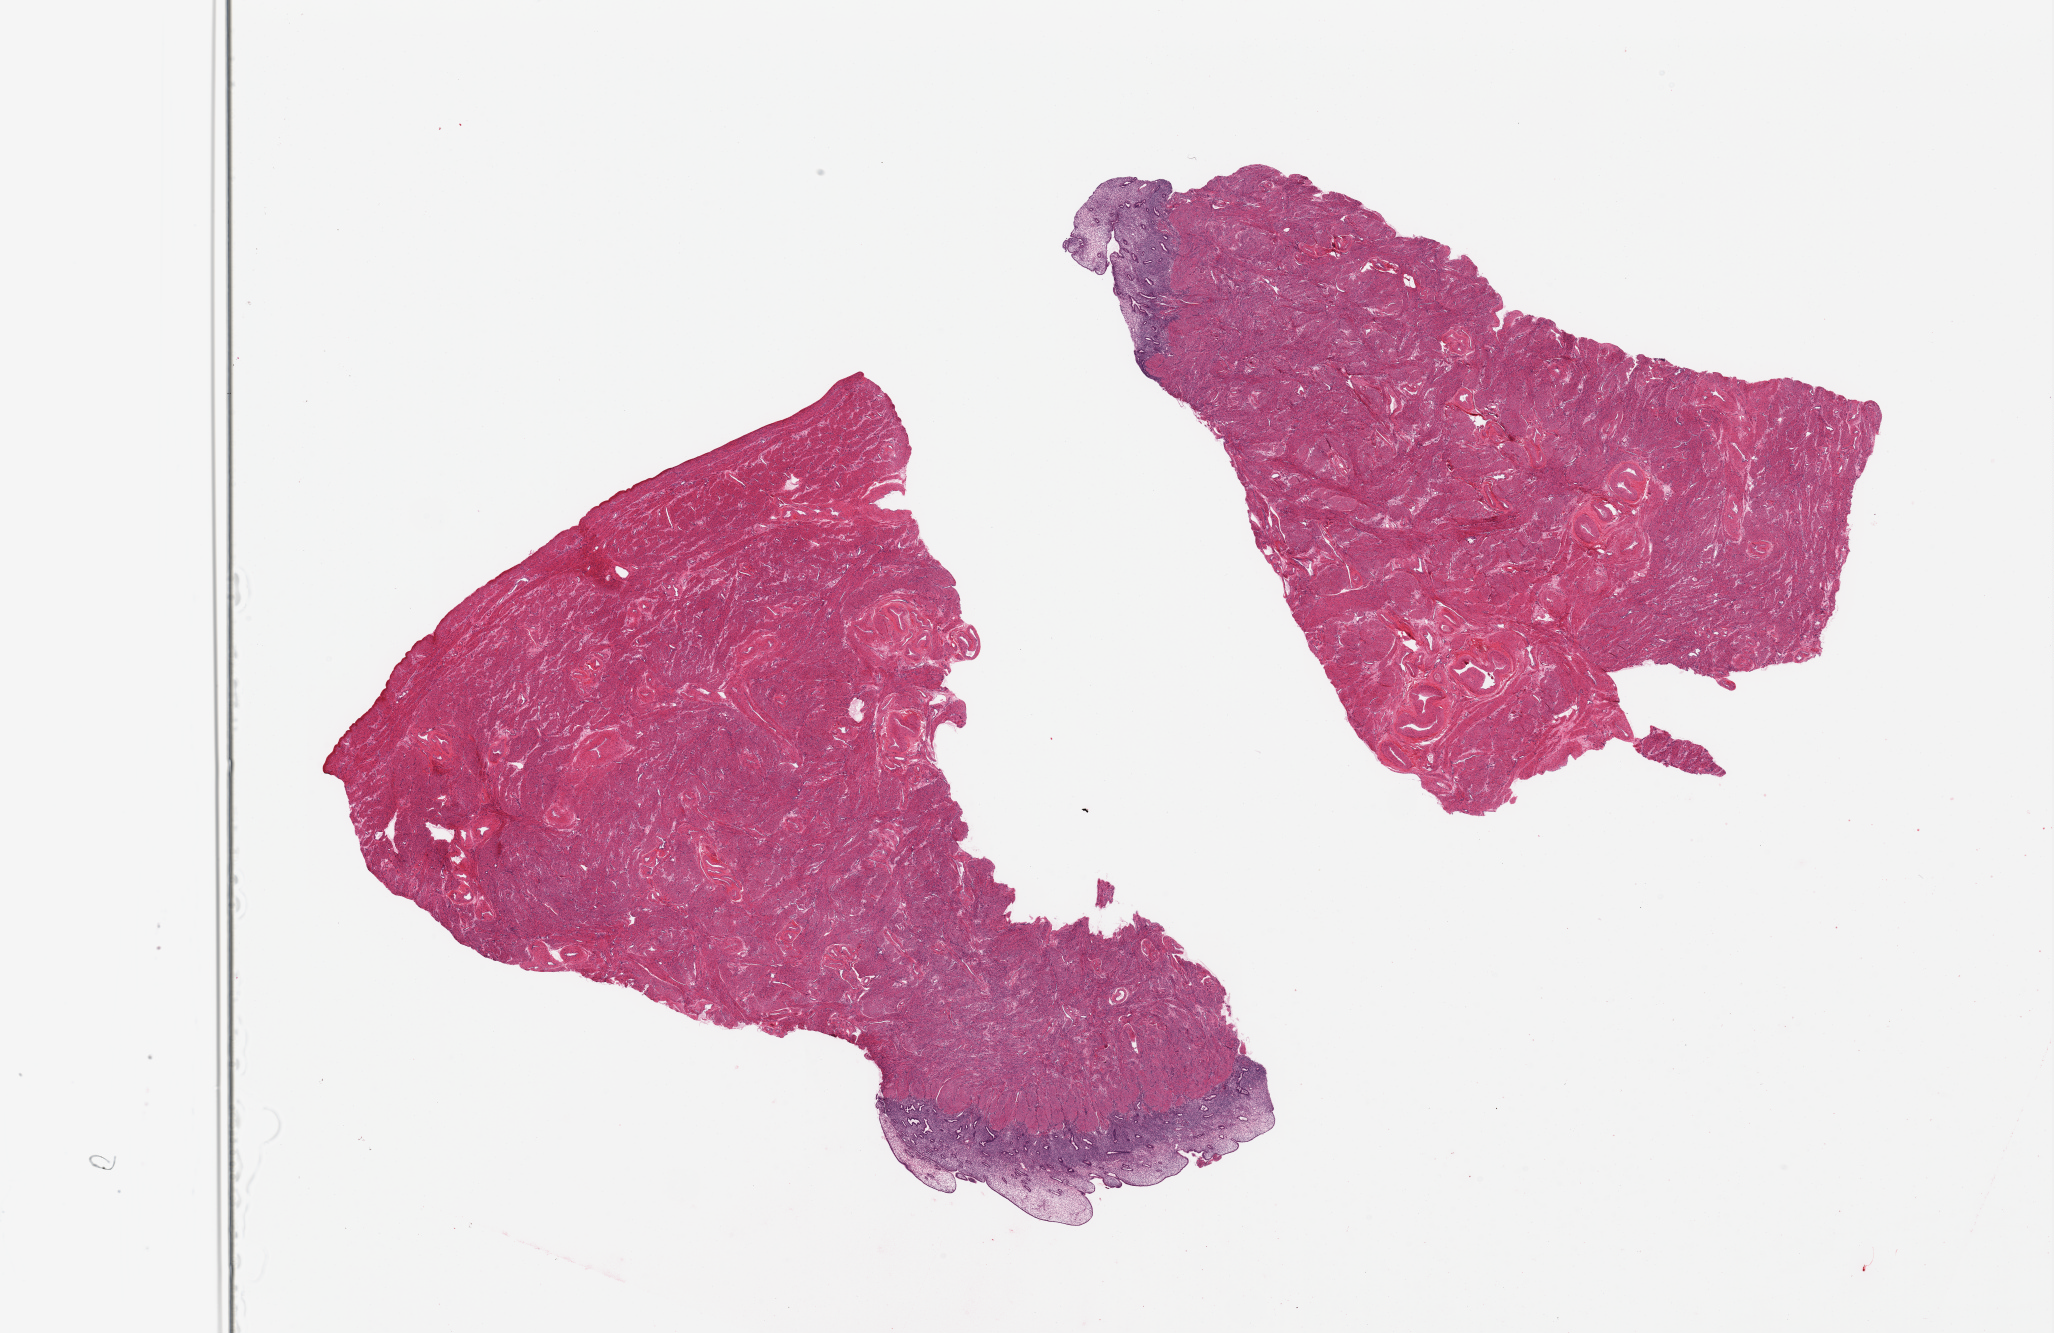
H&E whole-slide image, a low-resolution overview of the entire scanned area, about 32.5 x 21.1 mm (from a 20x scan), PAXgene-fixed paraffin-embedded (PFPE) section, target tissue: uterus, tissue donor sample.
Reviewer comment on this tissue sample: 2 pieces; myometrium and ~10% endometrium.